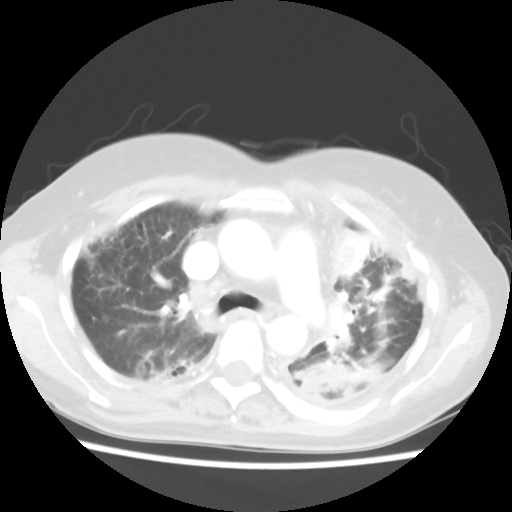
Chest CT, one axial slice. Slice 39 of 56 in the series (ordered by position). Lung window (W 1500 / L -600 HU). 5 mm slice thickness. 512 × 512 image matrix. Patient: female, 56 years. From the clinical record (not read from this slice): clinical TNM (as recorded): T1c N0 M1.
Outlined on this slice (rectangle marked by the reading radiologist):
- lung tumour (recorded histology: adenocarcinoma): bounding box <323,223,375,286> (left, top, right, bottom; pixels)